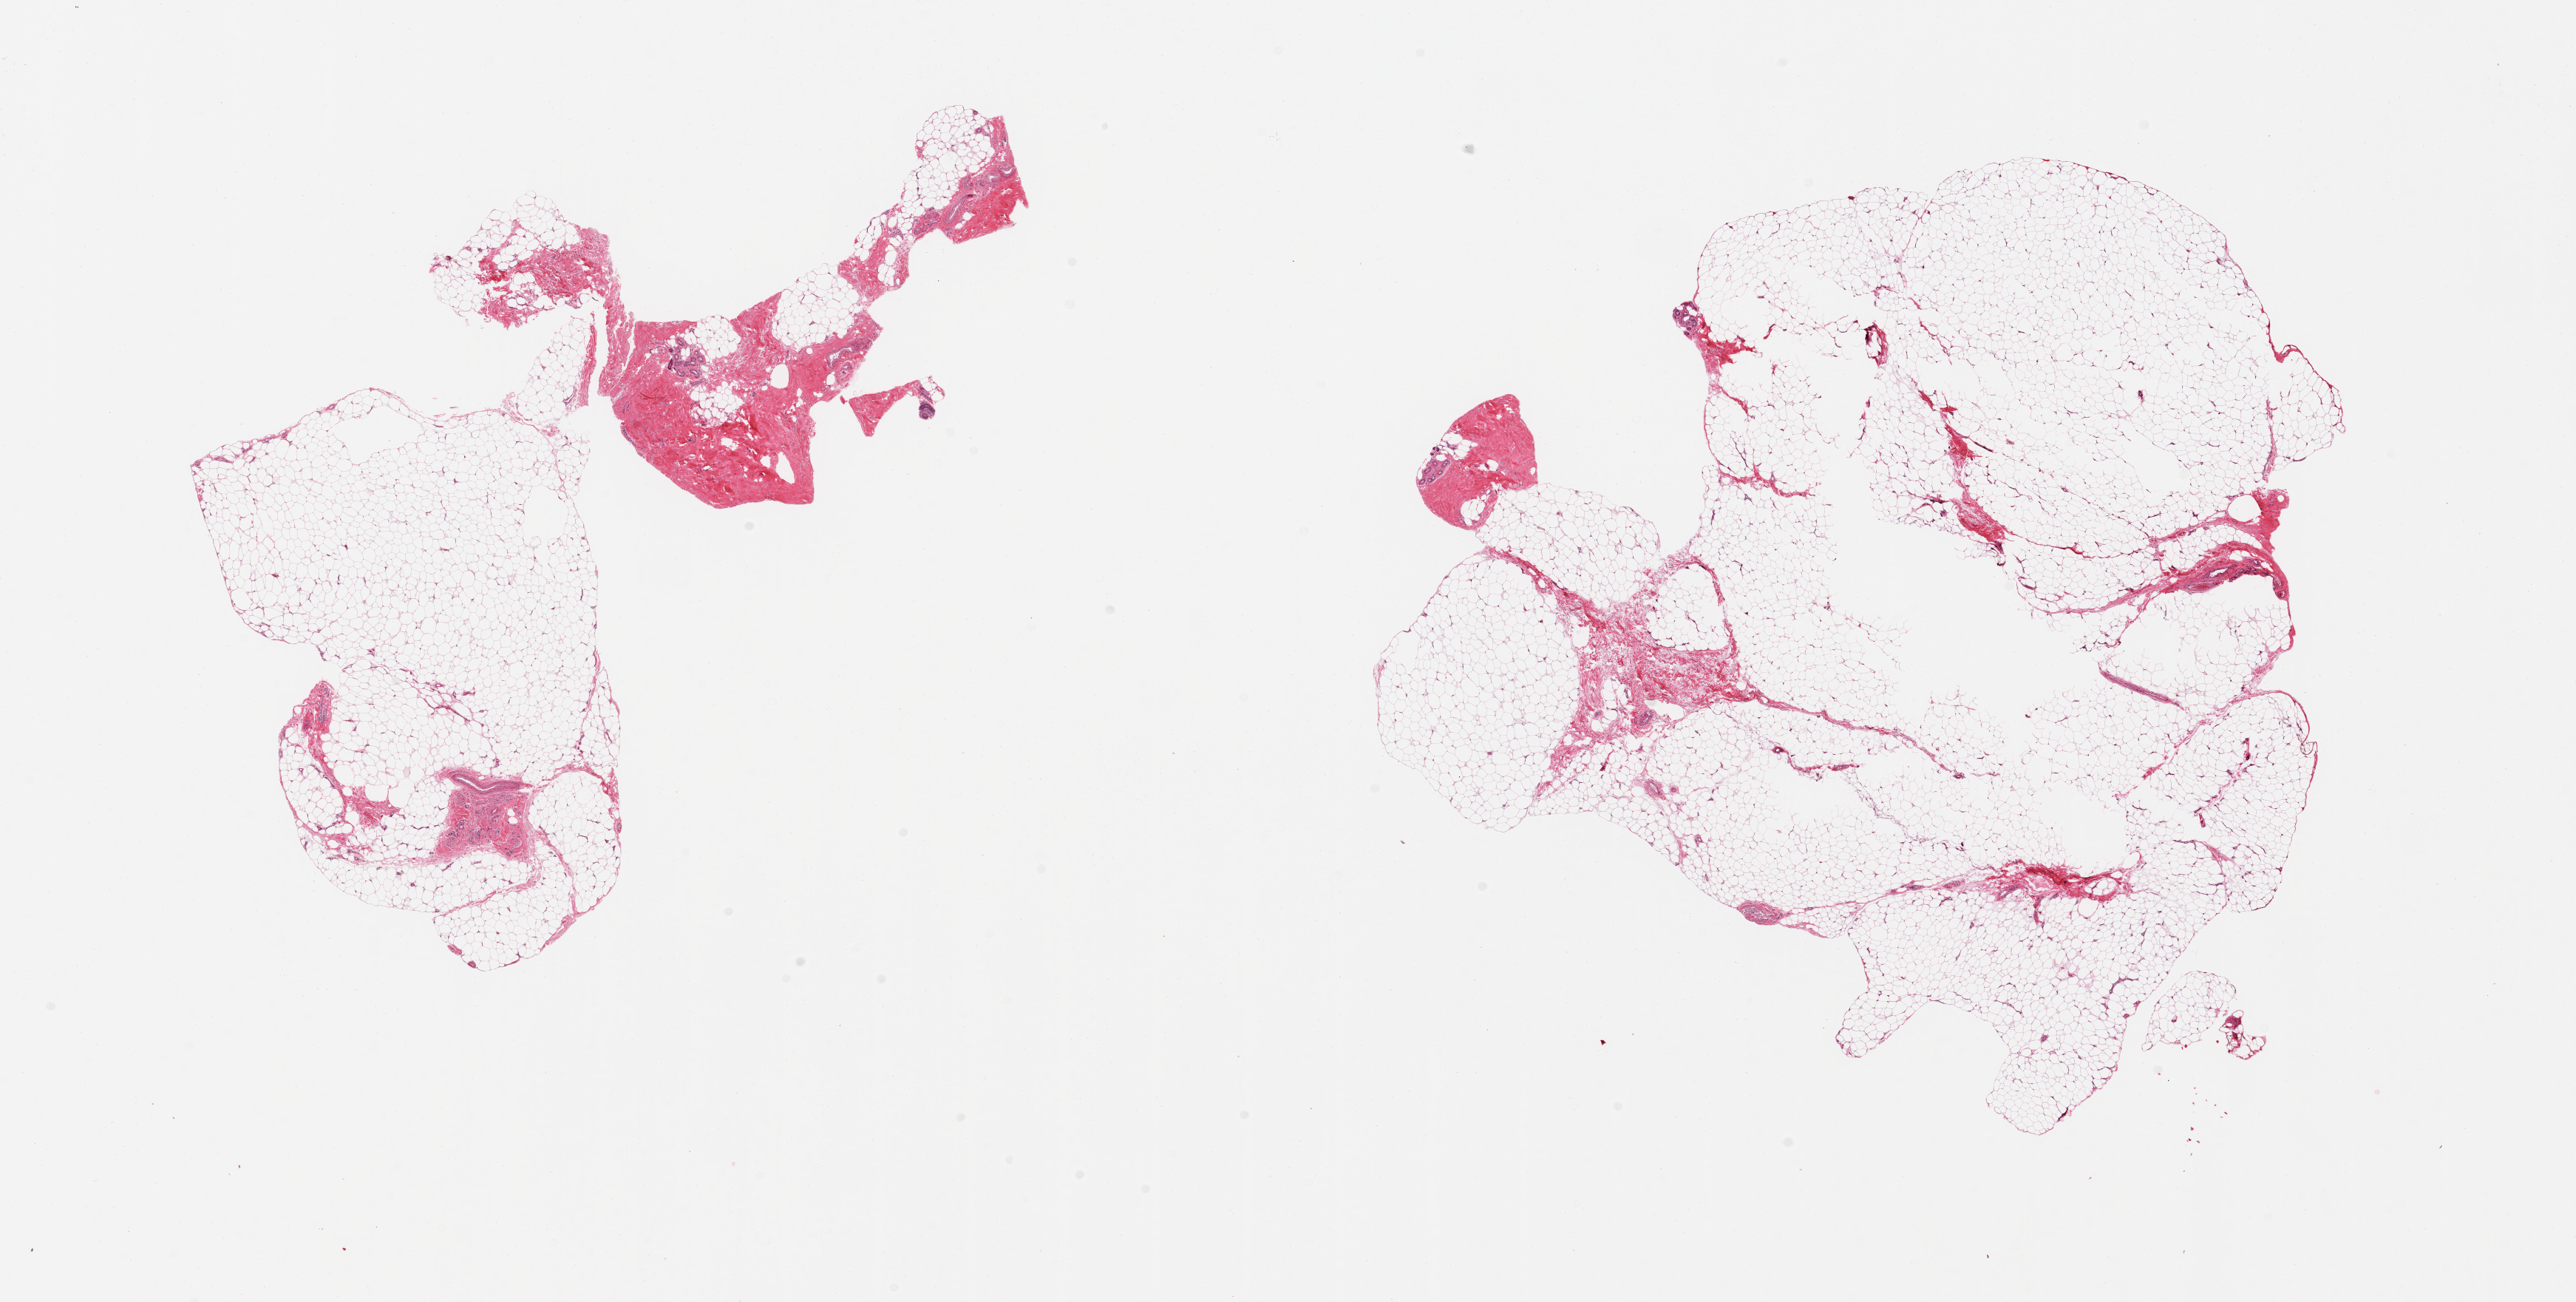
Whole-slide image, H&E stain, brightfield, low-resolution overview of the scanned area, about 27.6 x 13.9 mm (acquisition: 20x scan), PAXgene-fixed paraffin-embedded (PFPE) section, sampled site (target tissue): adipose tissue, tissue donor sample. Male donor.
Reviewer comment on this tissue sample: 2 pieces; fascia/vascular elements are ~20% of tissue.